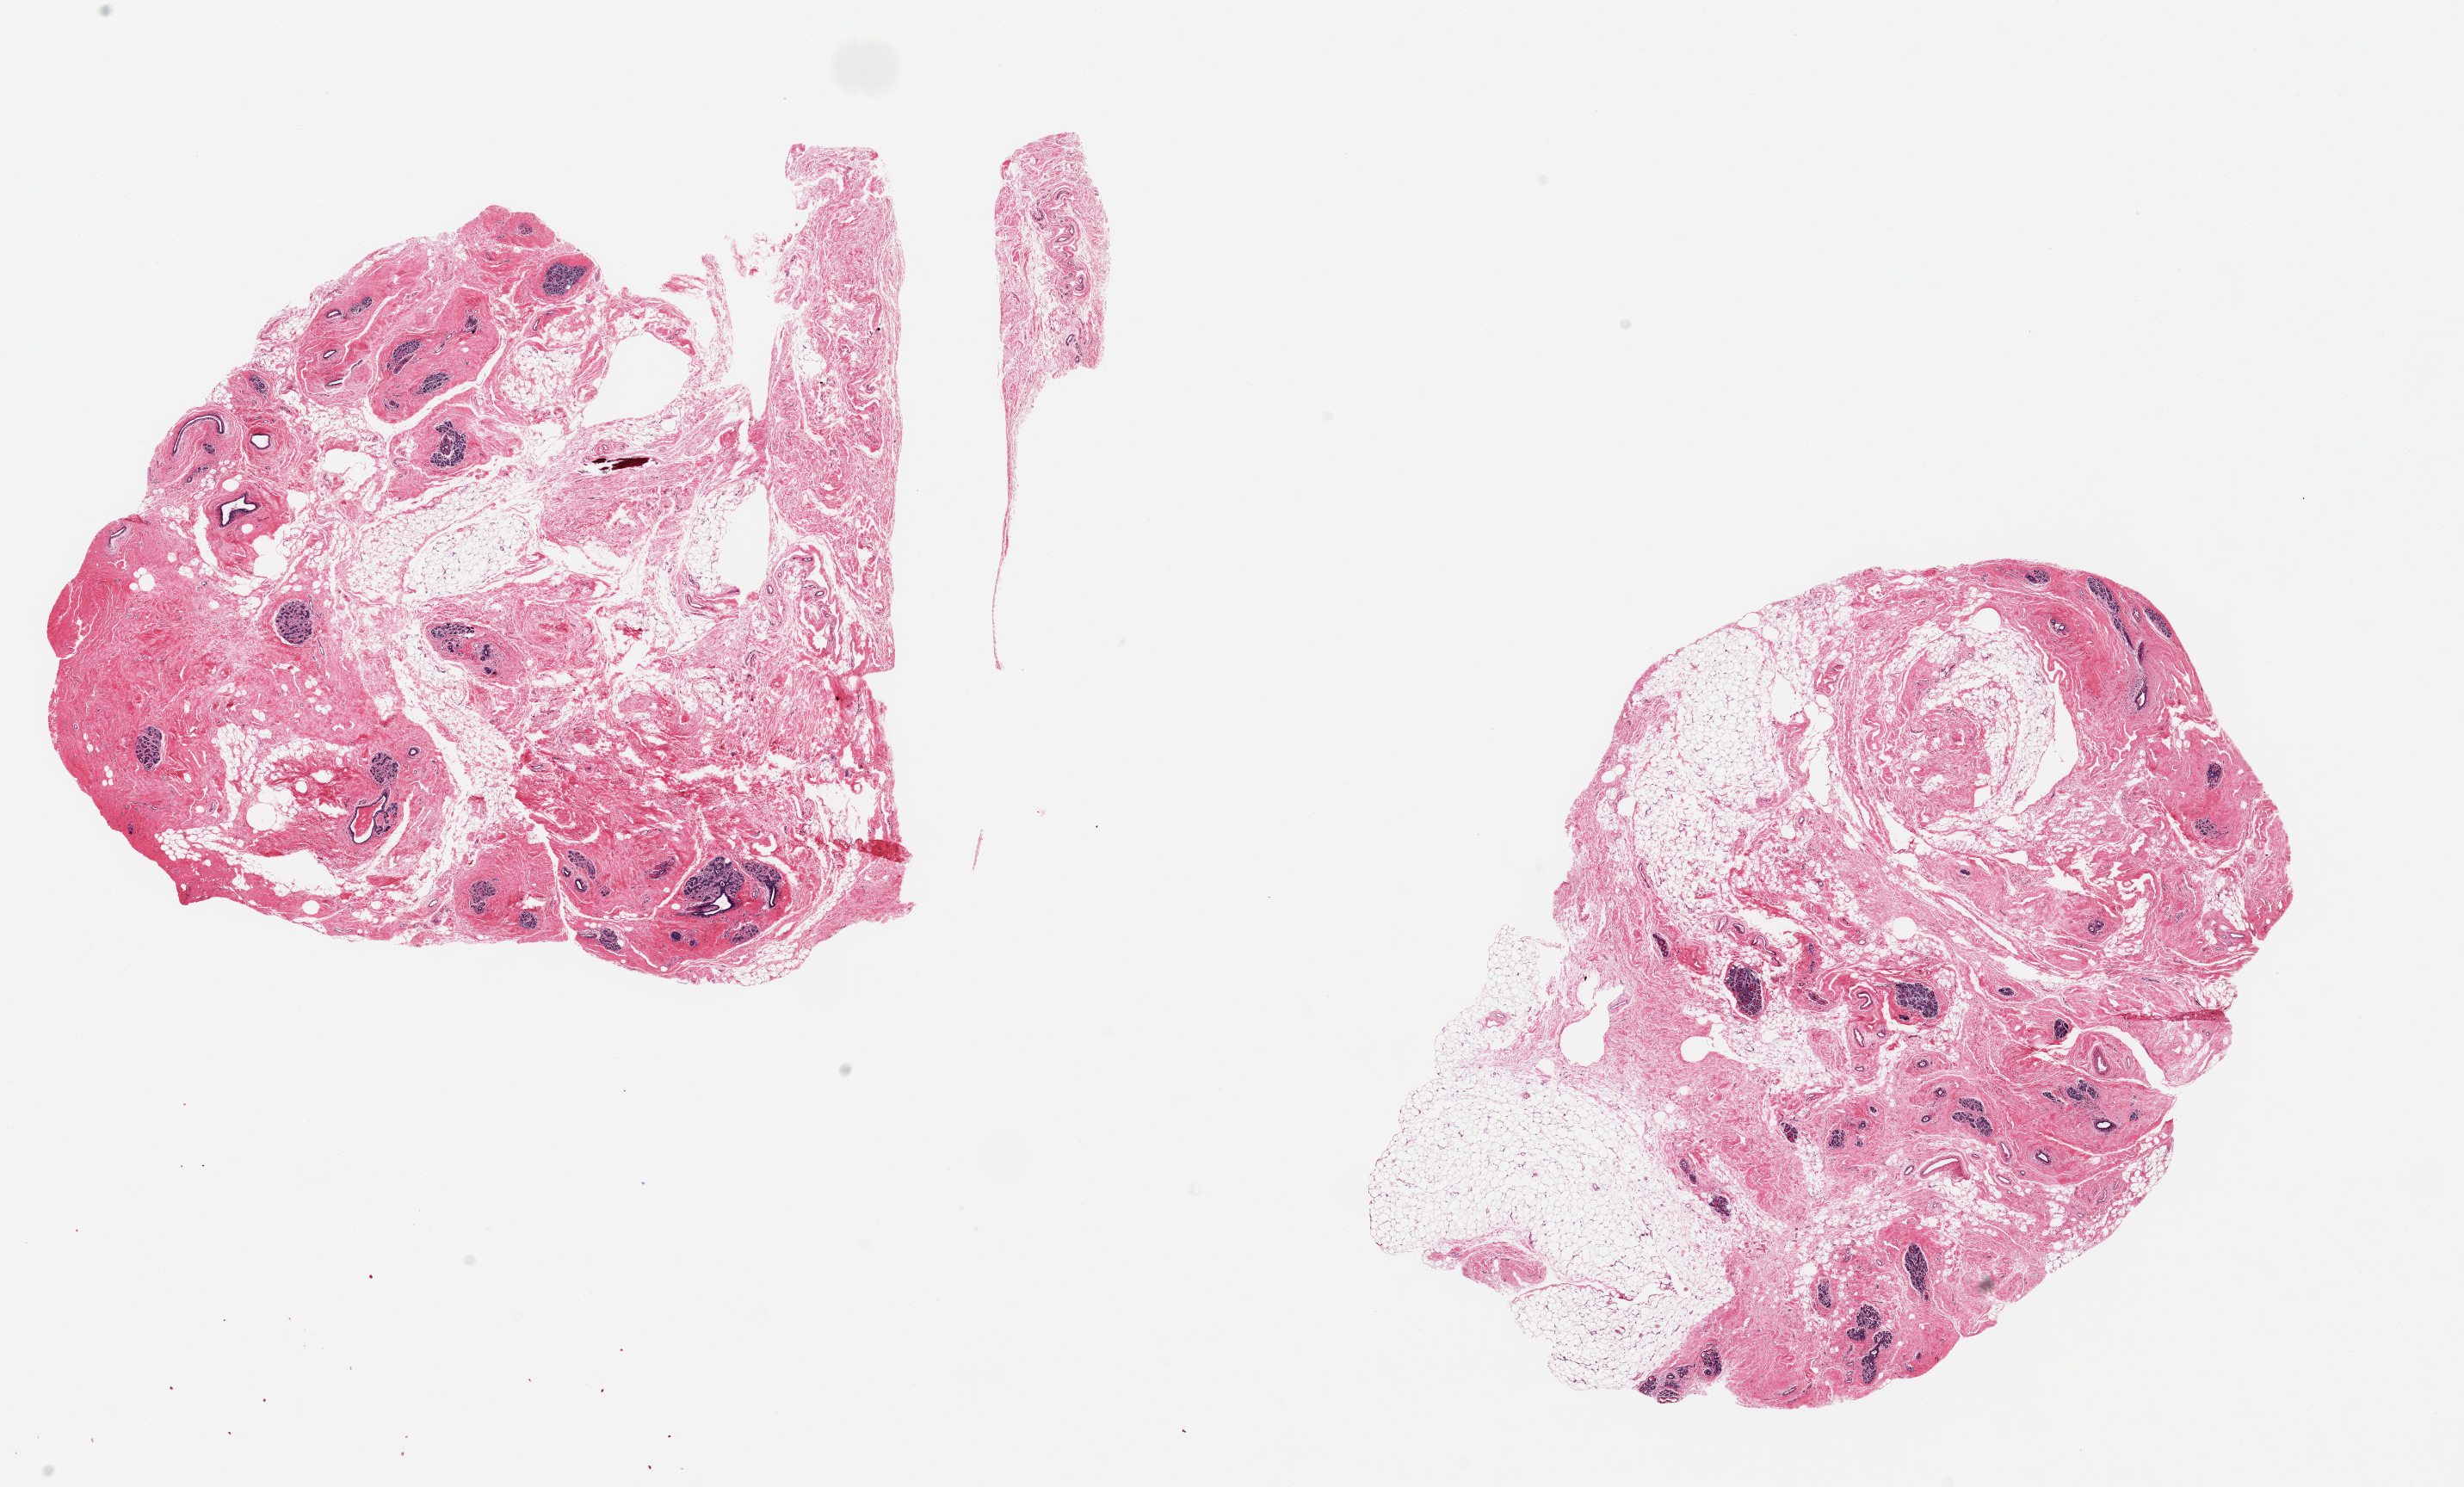
Haematoxylin and eosin whole-slide image, shown as a low-resolution overview of the whole scanned area (about 22.6 x 13.7 mm), PAXgene-fixed paraffin-embedded (PFPE) section, target tissue: breast, donor tissue sample.
Pathologist's review note for this sample: 2 pieces, 9x6 & 8x7mm; numerous terminal ducts and lobules; stroma is more fibrous than fatty.